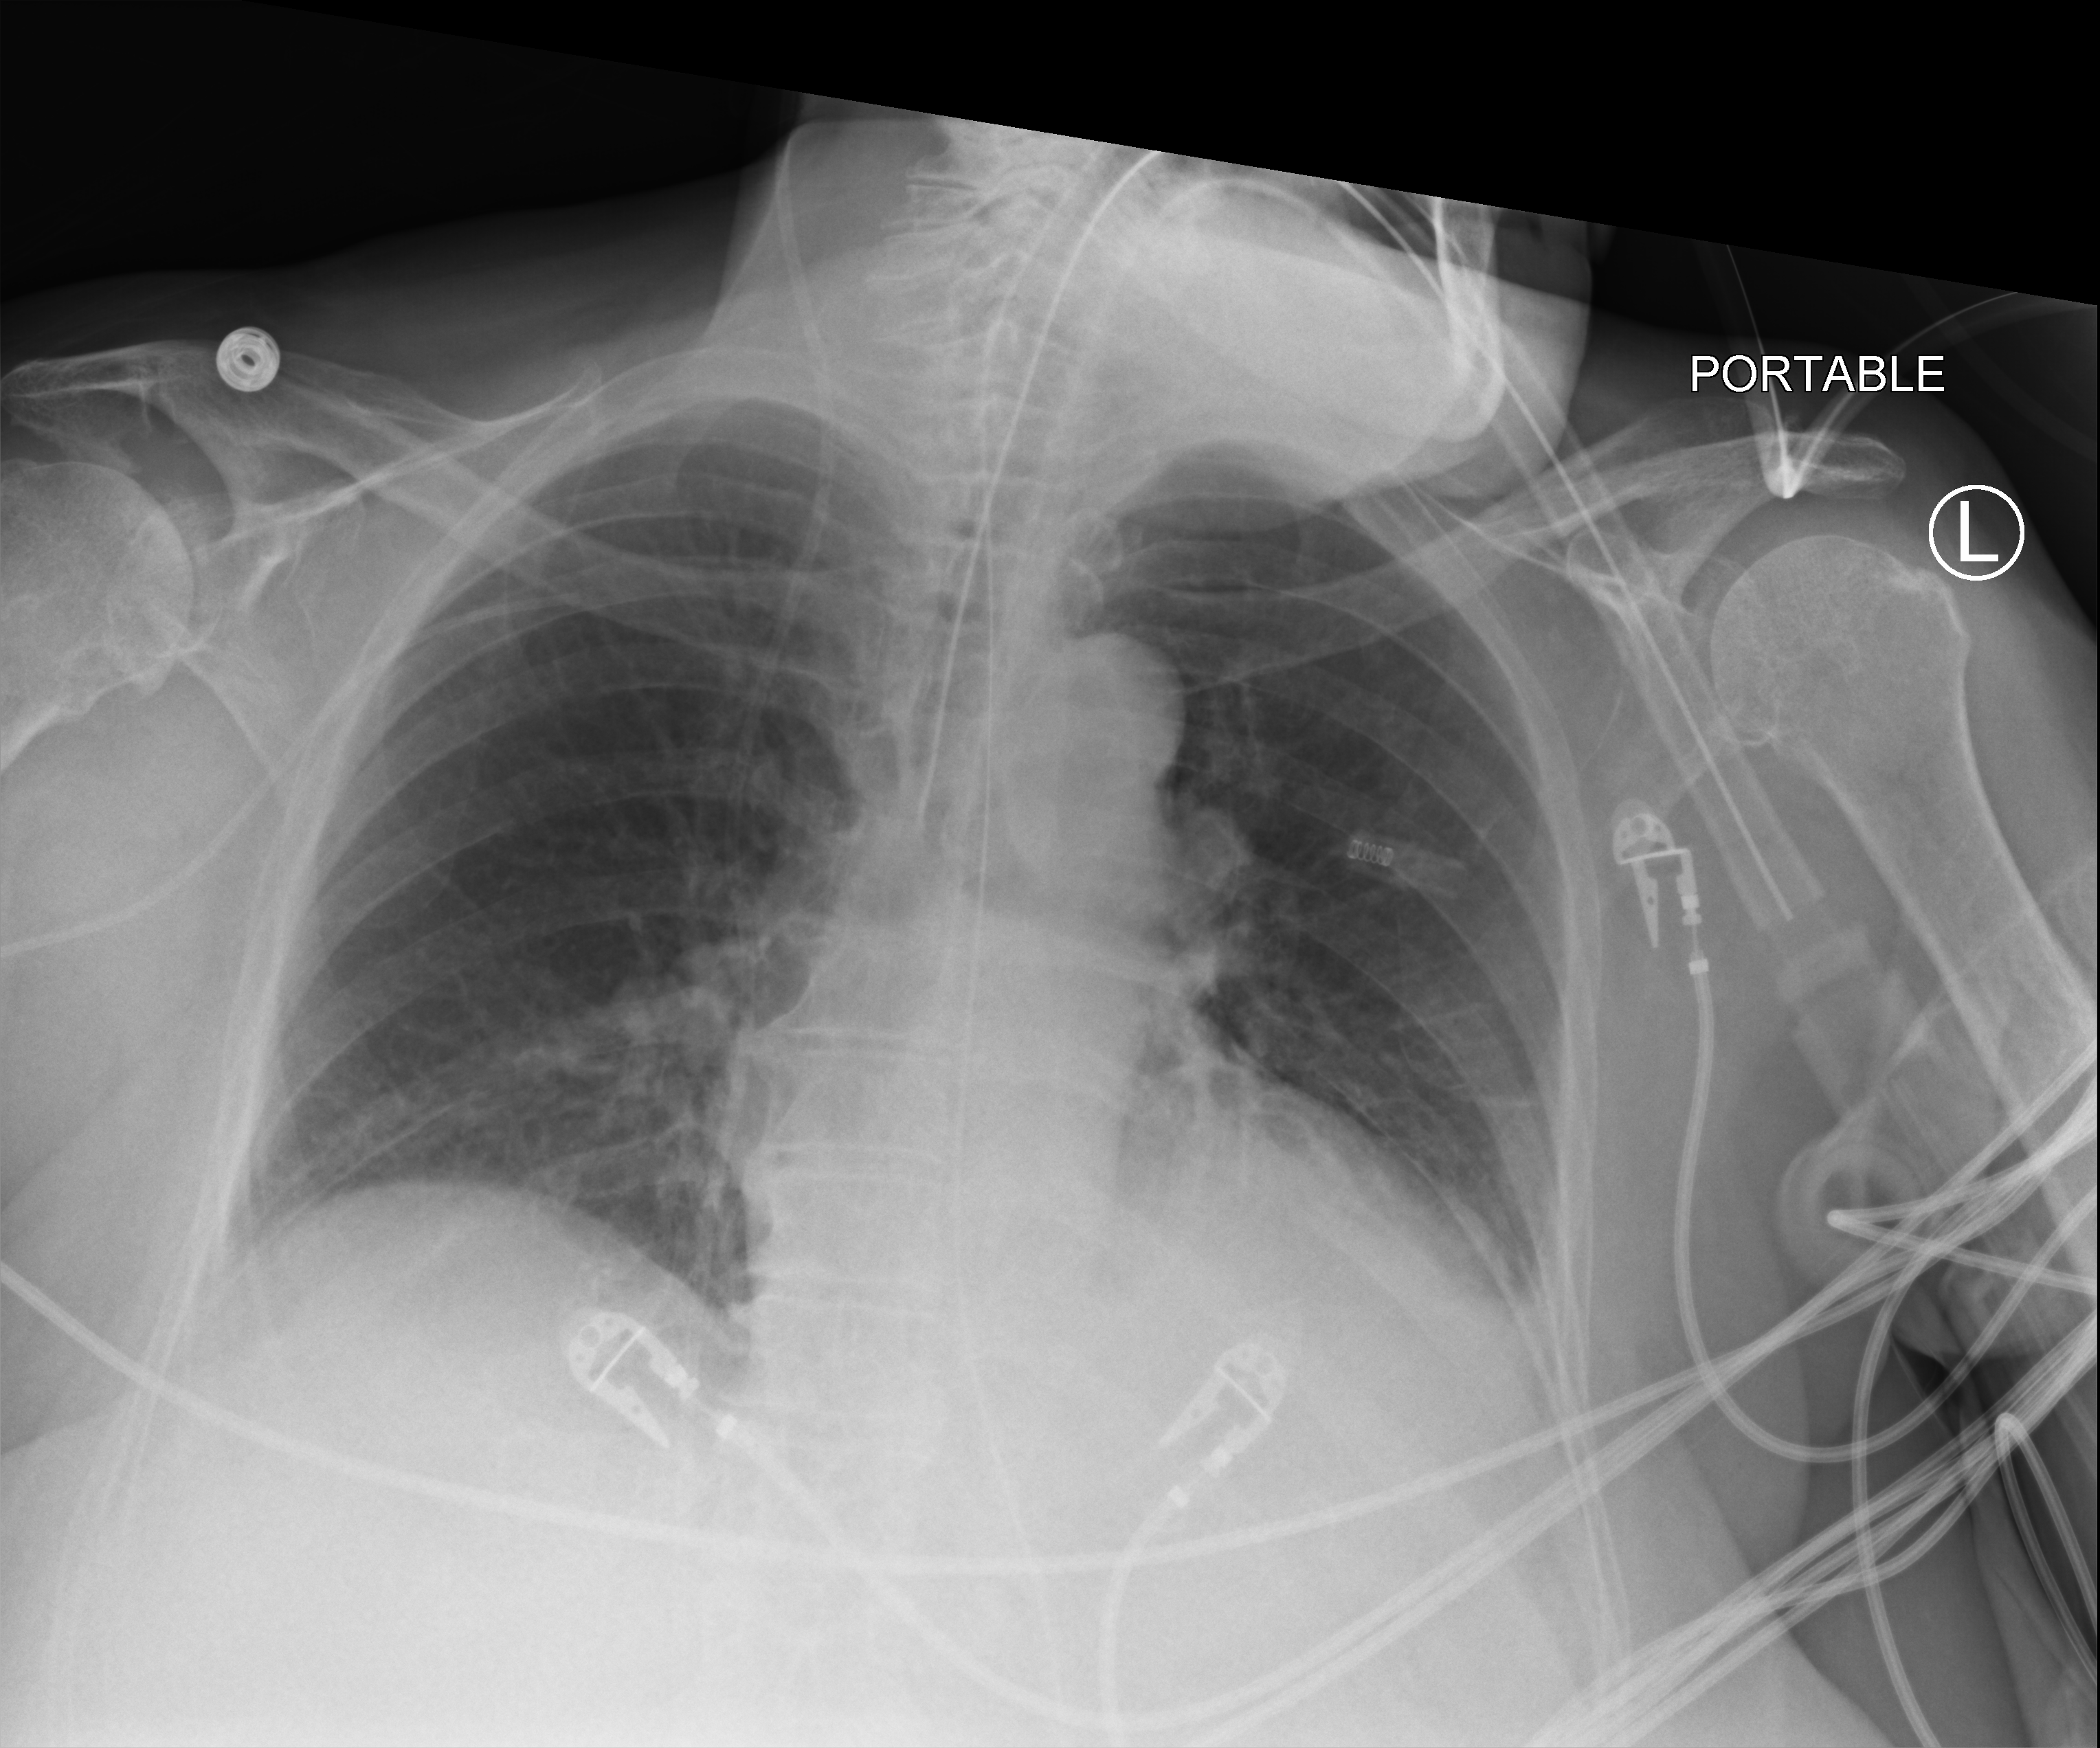
Chest X-ray (portable), anteroposterior (AP) projection. Patient hospitalised with COVID-19; female, aged 75–90 years.
Admission-level facts for this patient (not findings on this image; timing relative to this image not recorded): admitted to intensive care during this hospital stay: yes; length of hospital stay: 29 days; smoking status (admission record): never.